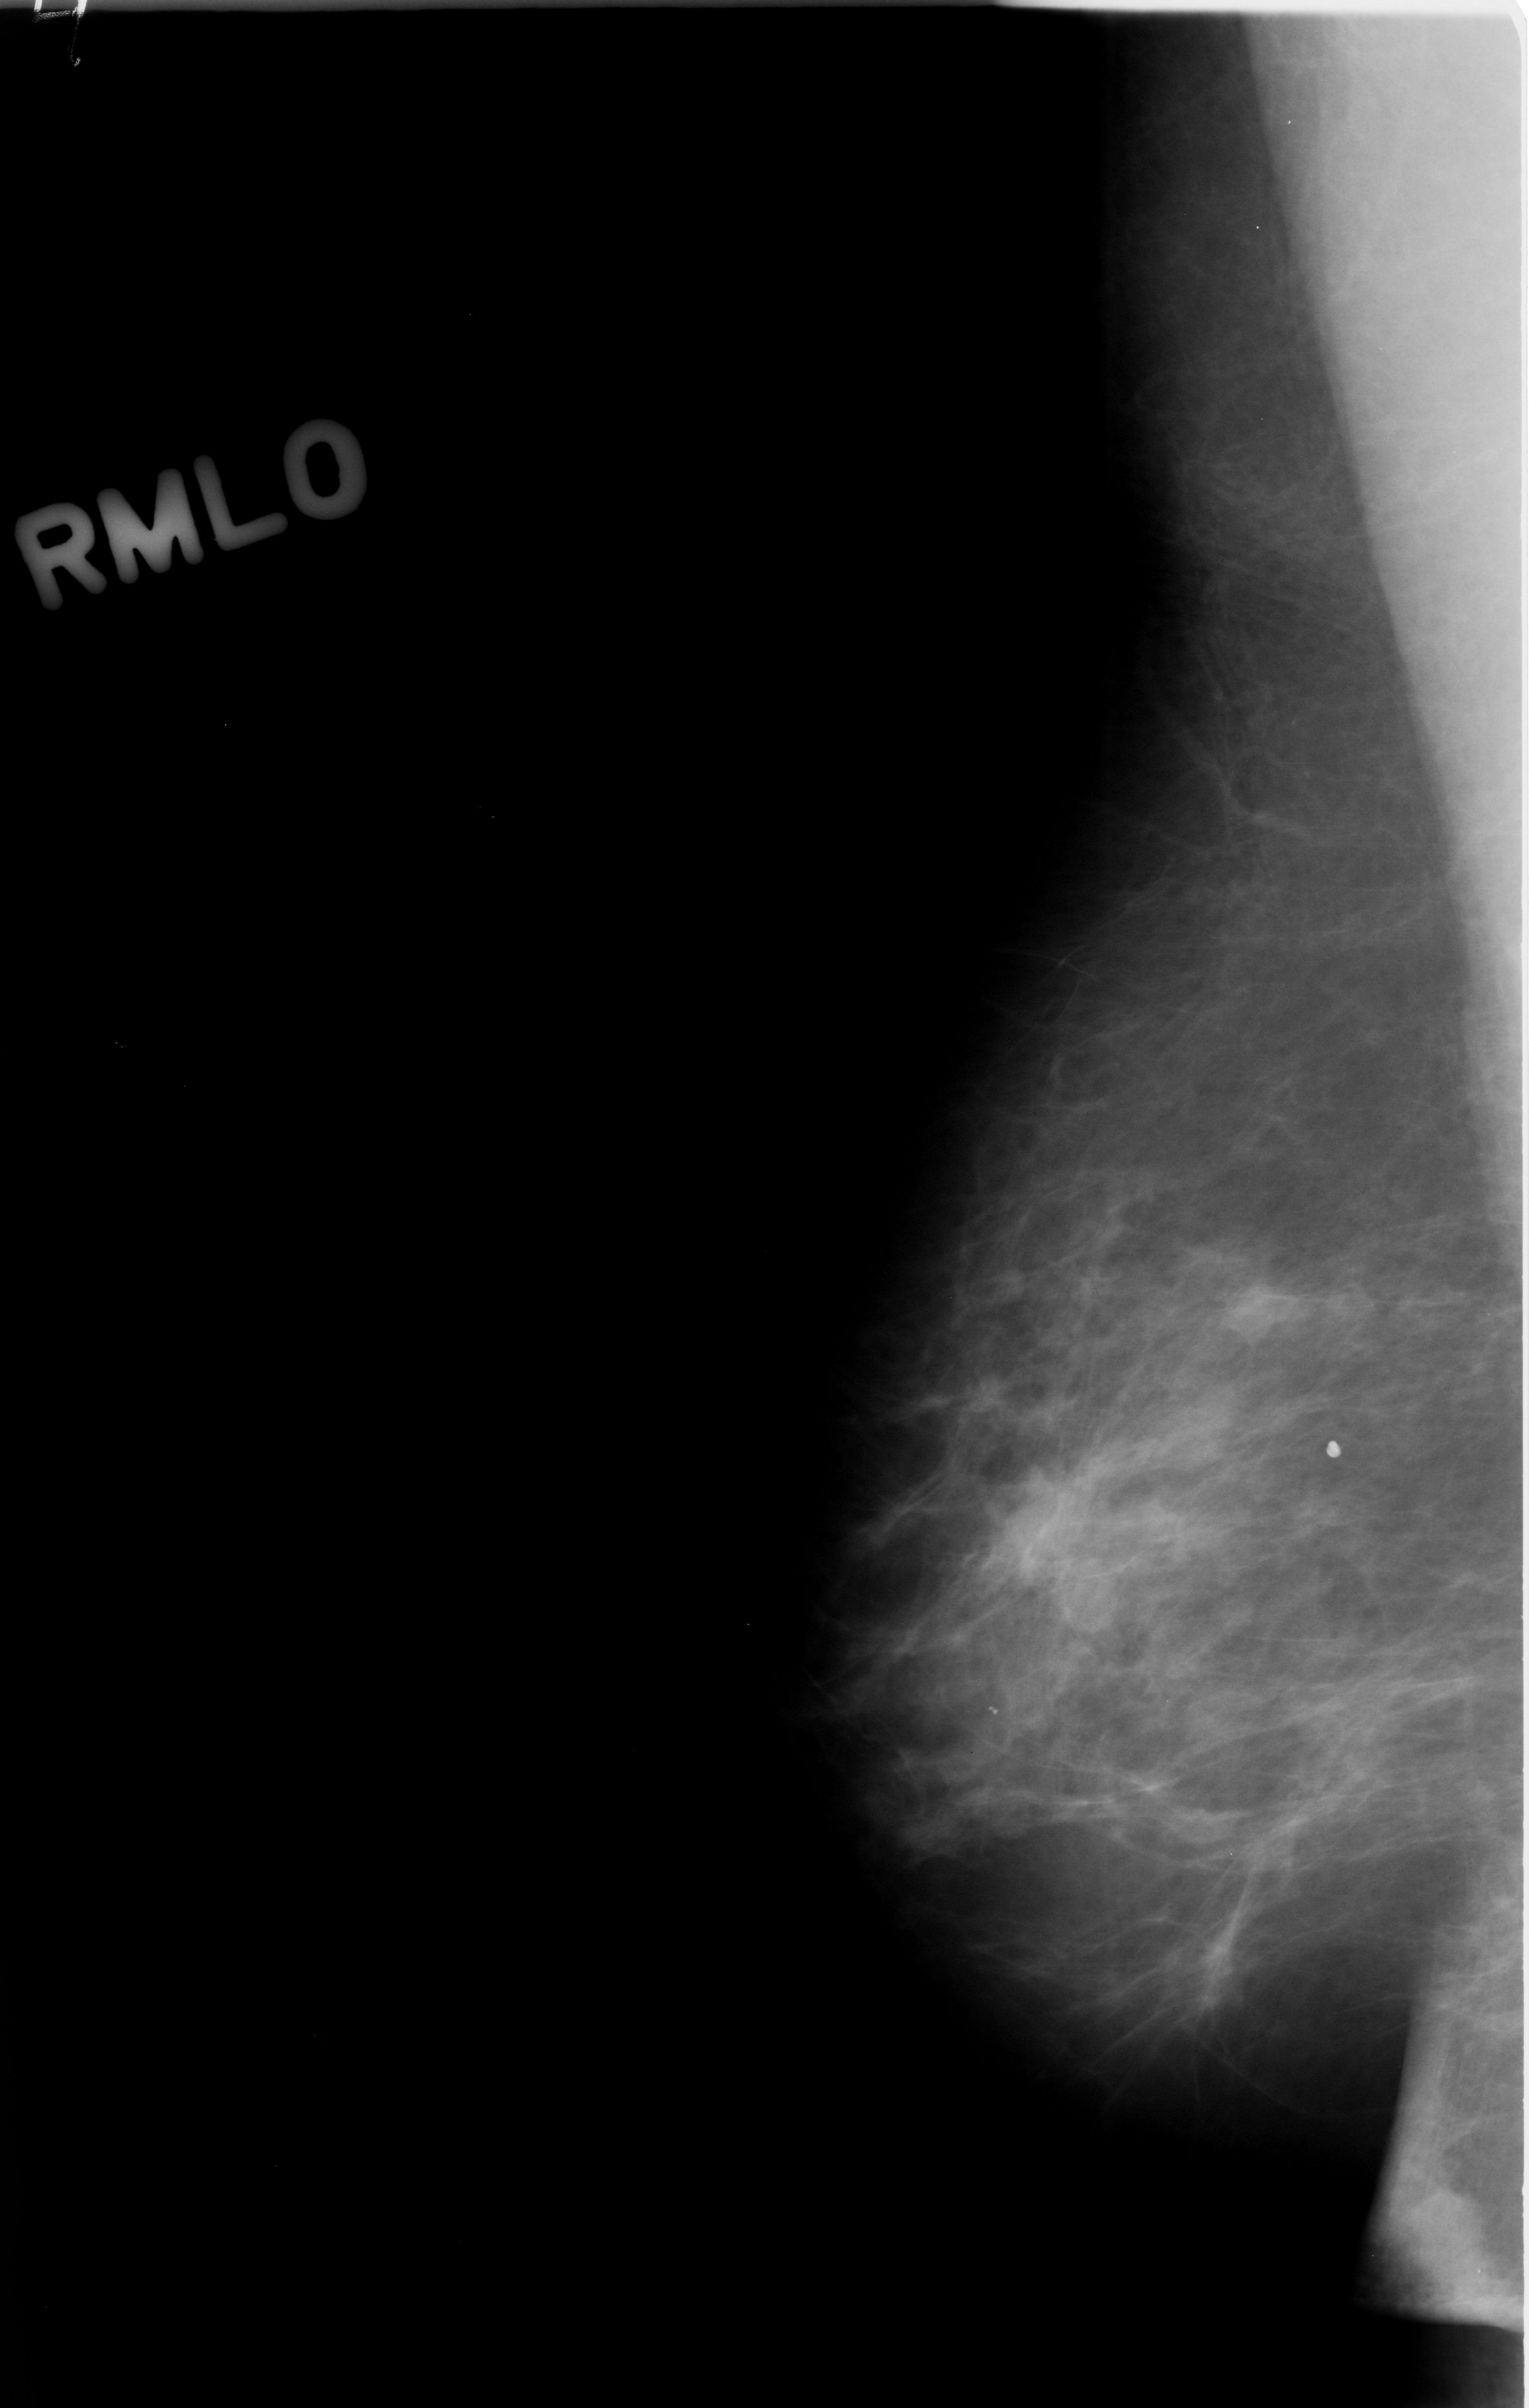
Mammogram (digitized film). Right breast. Mediolateral oblique (MLO) view. Breast composition: scattered fibroglandular densities (BI-RADS density category 2 of 4). 1529 × 2408 image matrix.
Expert-marked regions of interest on this film, with their recorded descriptors:
- mass, shape oval, margins circumscribed; BI-RADS assessment category 3; subtlety rating 4 on a 1 (subtle) to 5 (obvious) scale; benign; no additional work-up was recommended (outcome (as recorded, no biopsy): benign without callback): bounding box (x1, y1, x2, y2) in pixels: (1041, 1529, 1144, 1642)